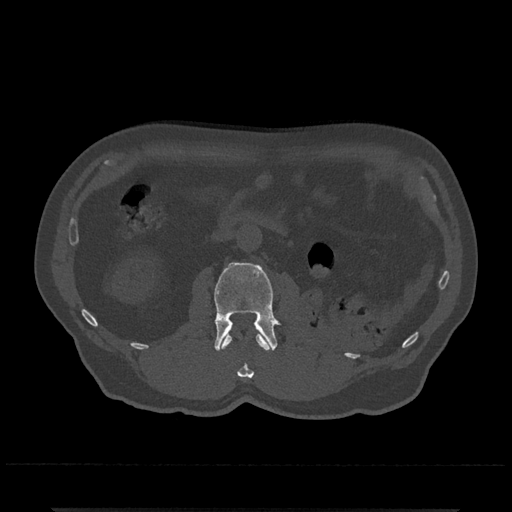
CT including the spine, one axial slice. Slice 309 of 797 in the series (ordered by position). Reconstruction kernel Br40s/3. 120 kVp. Bone window (W 1800 / L 400 HU). 512 × 512 image matrix. Male patient, age 67 years. Case-level facts recorded for this patient, not image findings: primary cancer: prostate.
Outlined on this slice (semi-automatically segmented with operator editing):
- L1 vertebra: bounding box (x1, y1, x2, y2) in pixels: (221, 333, 270, 378)
- L2 vertebra: (214, 262, 283, 351)